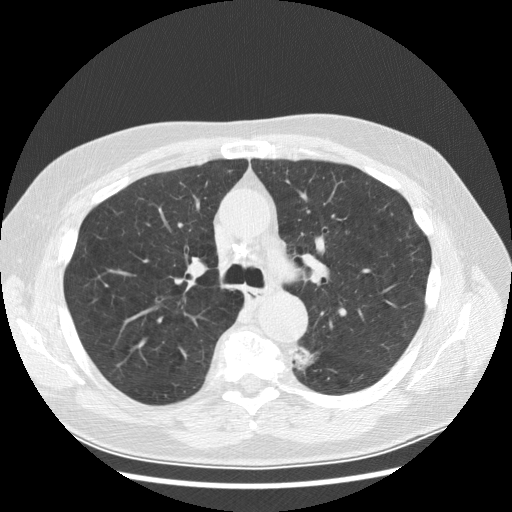
Low-dose screening chest CT, one axial slice; position 191 of 282 along the scan axis; reconstruction kernel STANDARD; 120 kVp; lung window (W 1500 / L -600 HU); 512 × 512 image matrix, field of view 370 × 370 mm.
Outlined on this slice (expert manual segmentation):
- lesion 1 (tumor, lower lobe of left lung): bounding box [x1, y1, x2, y2] px = [294, 346, 314, 371]